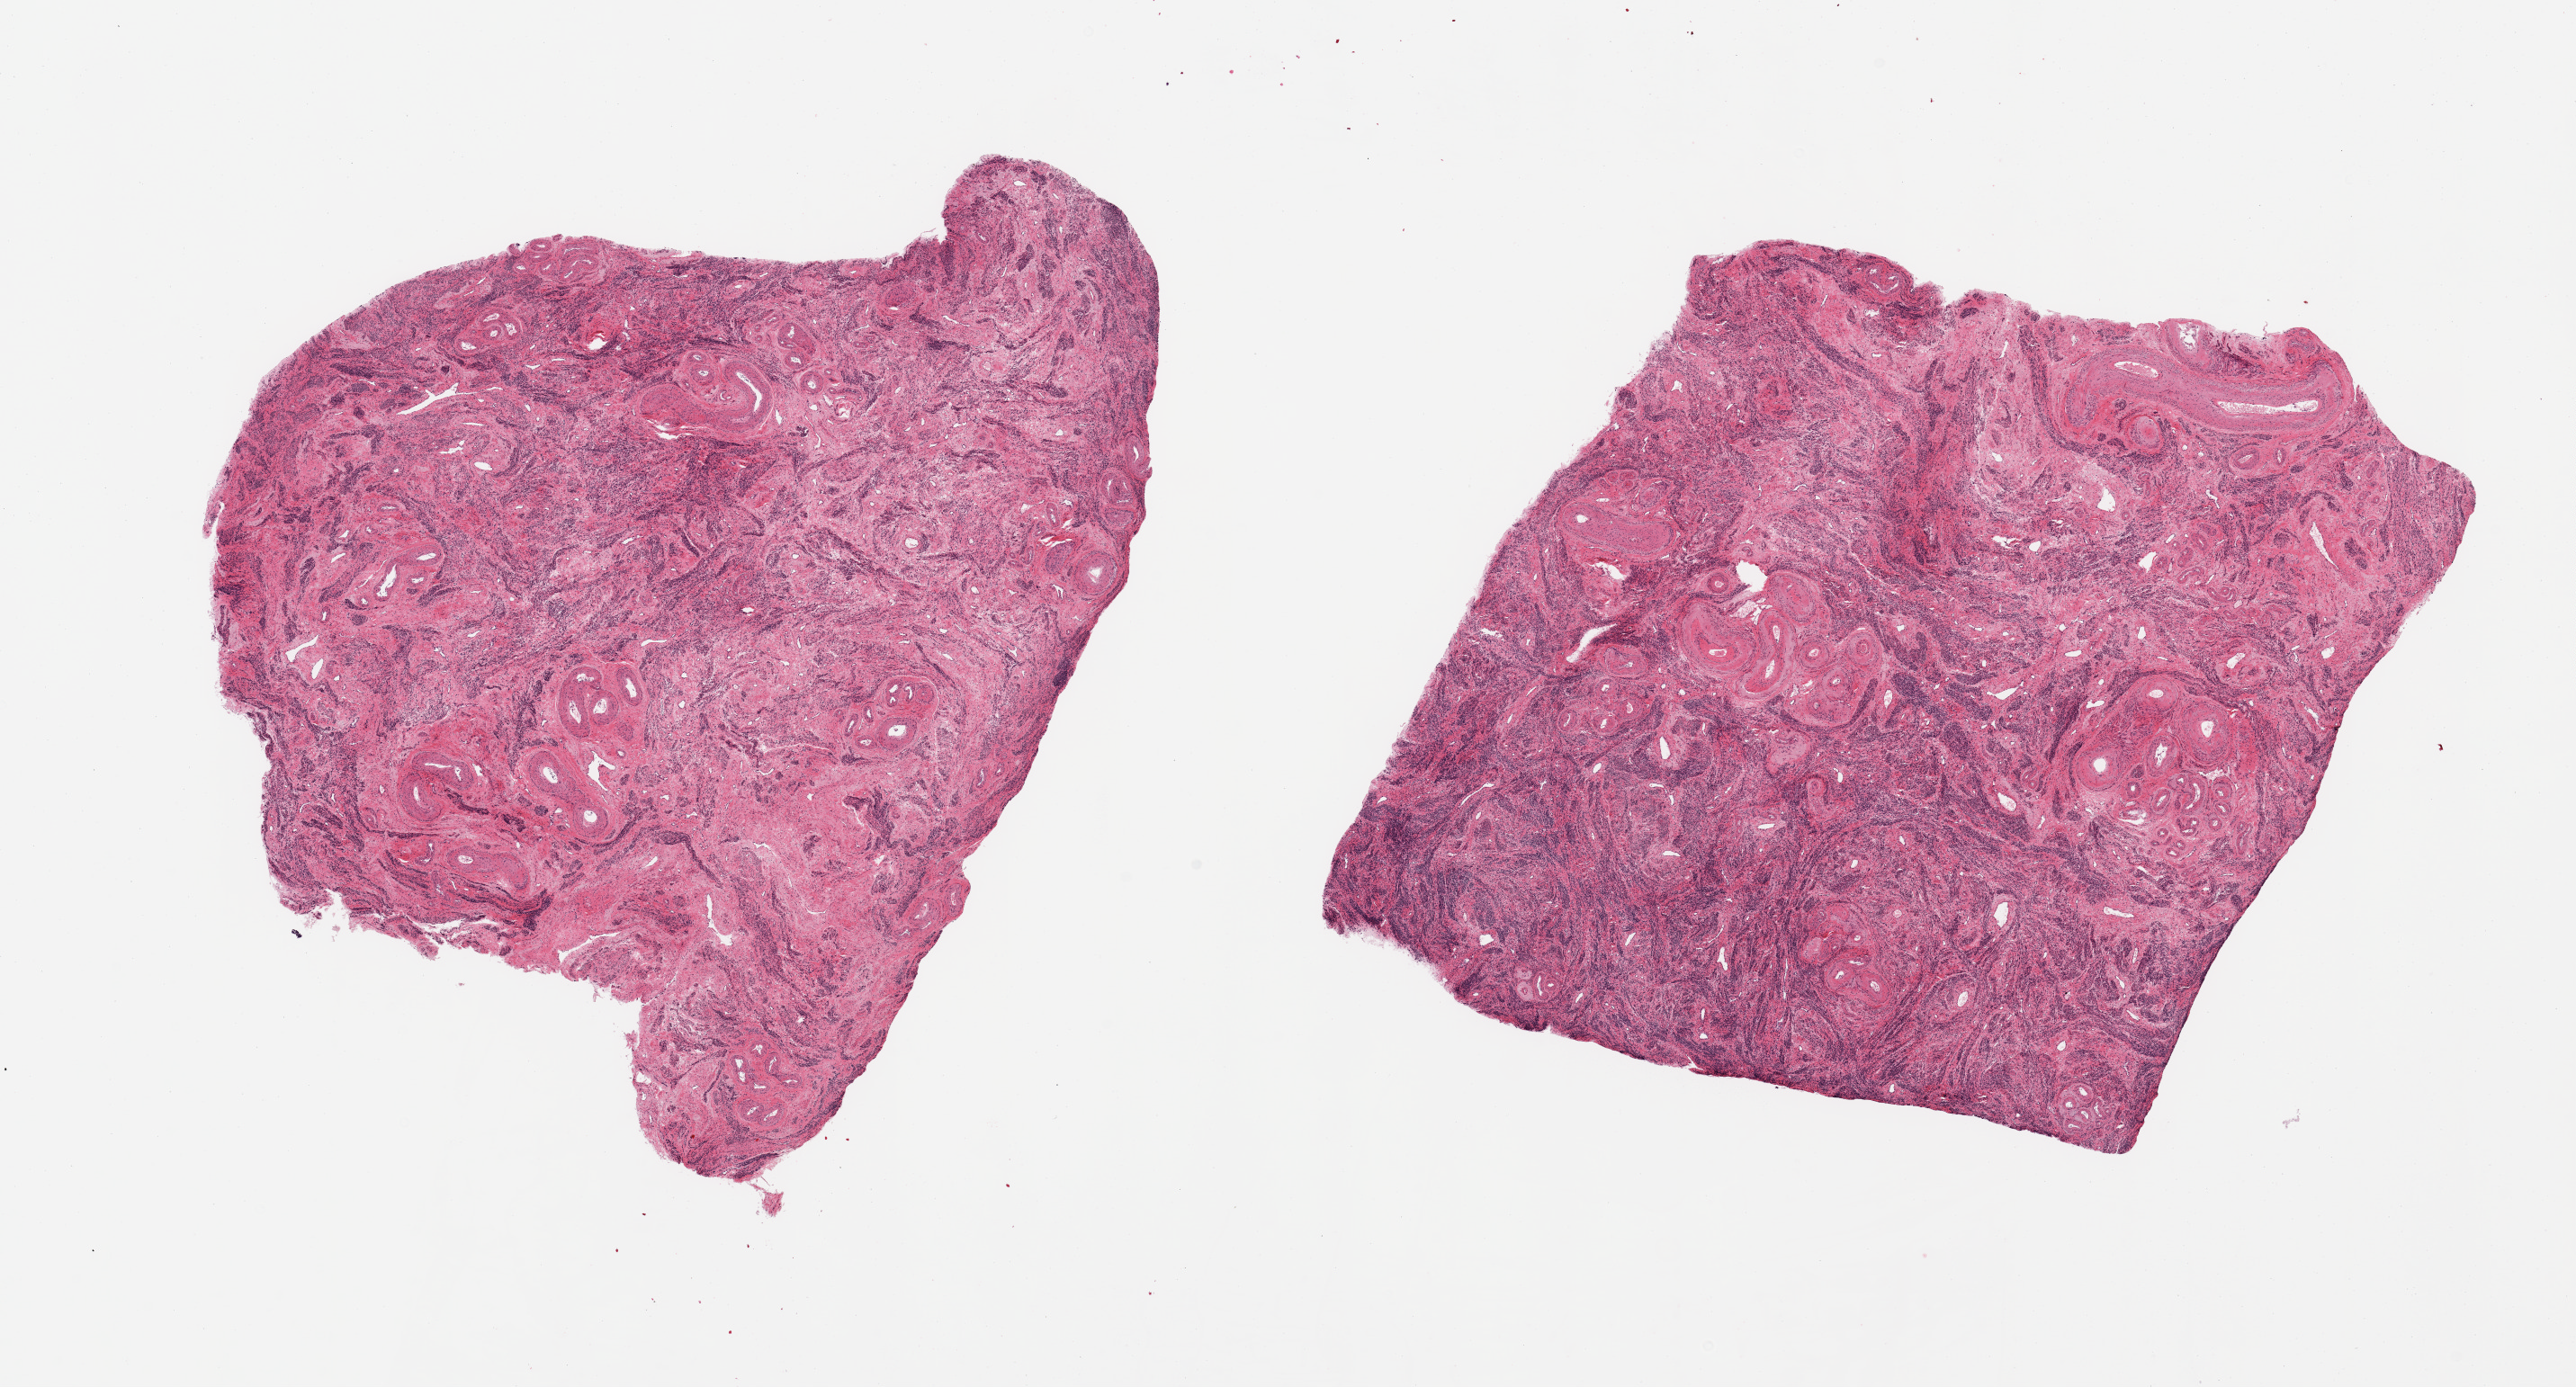
Whole-slide image, hematoxylin and eosin (H&E) stain — a low-resolution overview of the entire scanned area, about 22.6 x 12.2 mm. PAXgene-fixed, paraffin-embedded tissue. Sampled site (target tissue): uterus. Donor tissue sample. Donor sex: female.
Review note (as recorded): 2 pieces; all myometrium (in these sections).